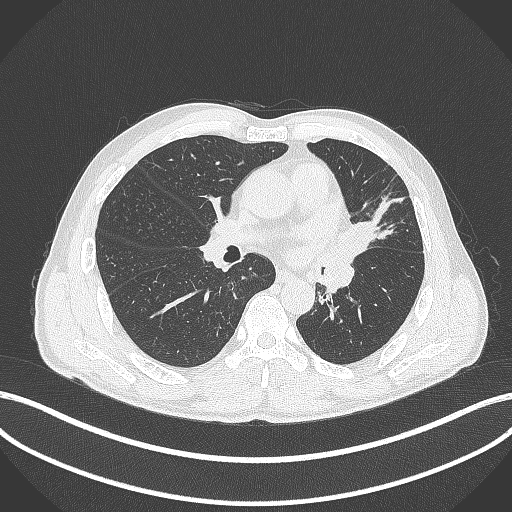
Chest CT, one axial slice. Slice 226 of 429 in the series (ordered by position). Reconstruction kernel B70f. Lung window (W 1500 / L -600 HU). 1 mm slice thickness. 512 × 512 image matrix. Male patient, age 57 years. From the clinical record (not read from this slice): clinical TNM (as recorded): T2b N0 M0.
Annotated regions visible in this slice (rectangle marked by the reading radiologist):
- lung tumour (recorded histology: squamous cell carcinoma): bounding box <333,219,374,264> (left, top, right, bottom; pixels)